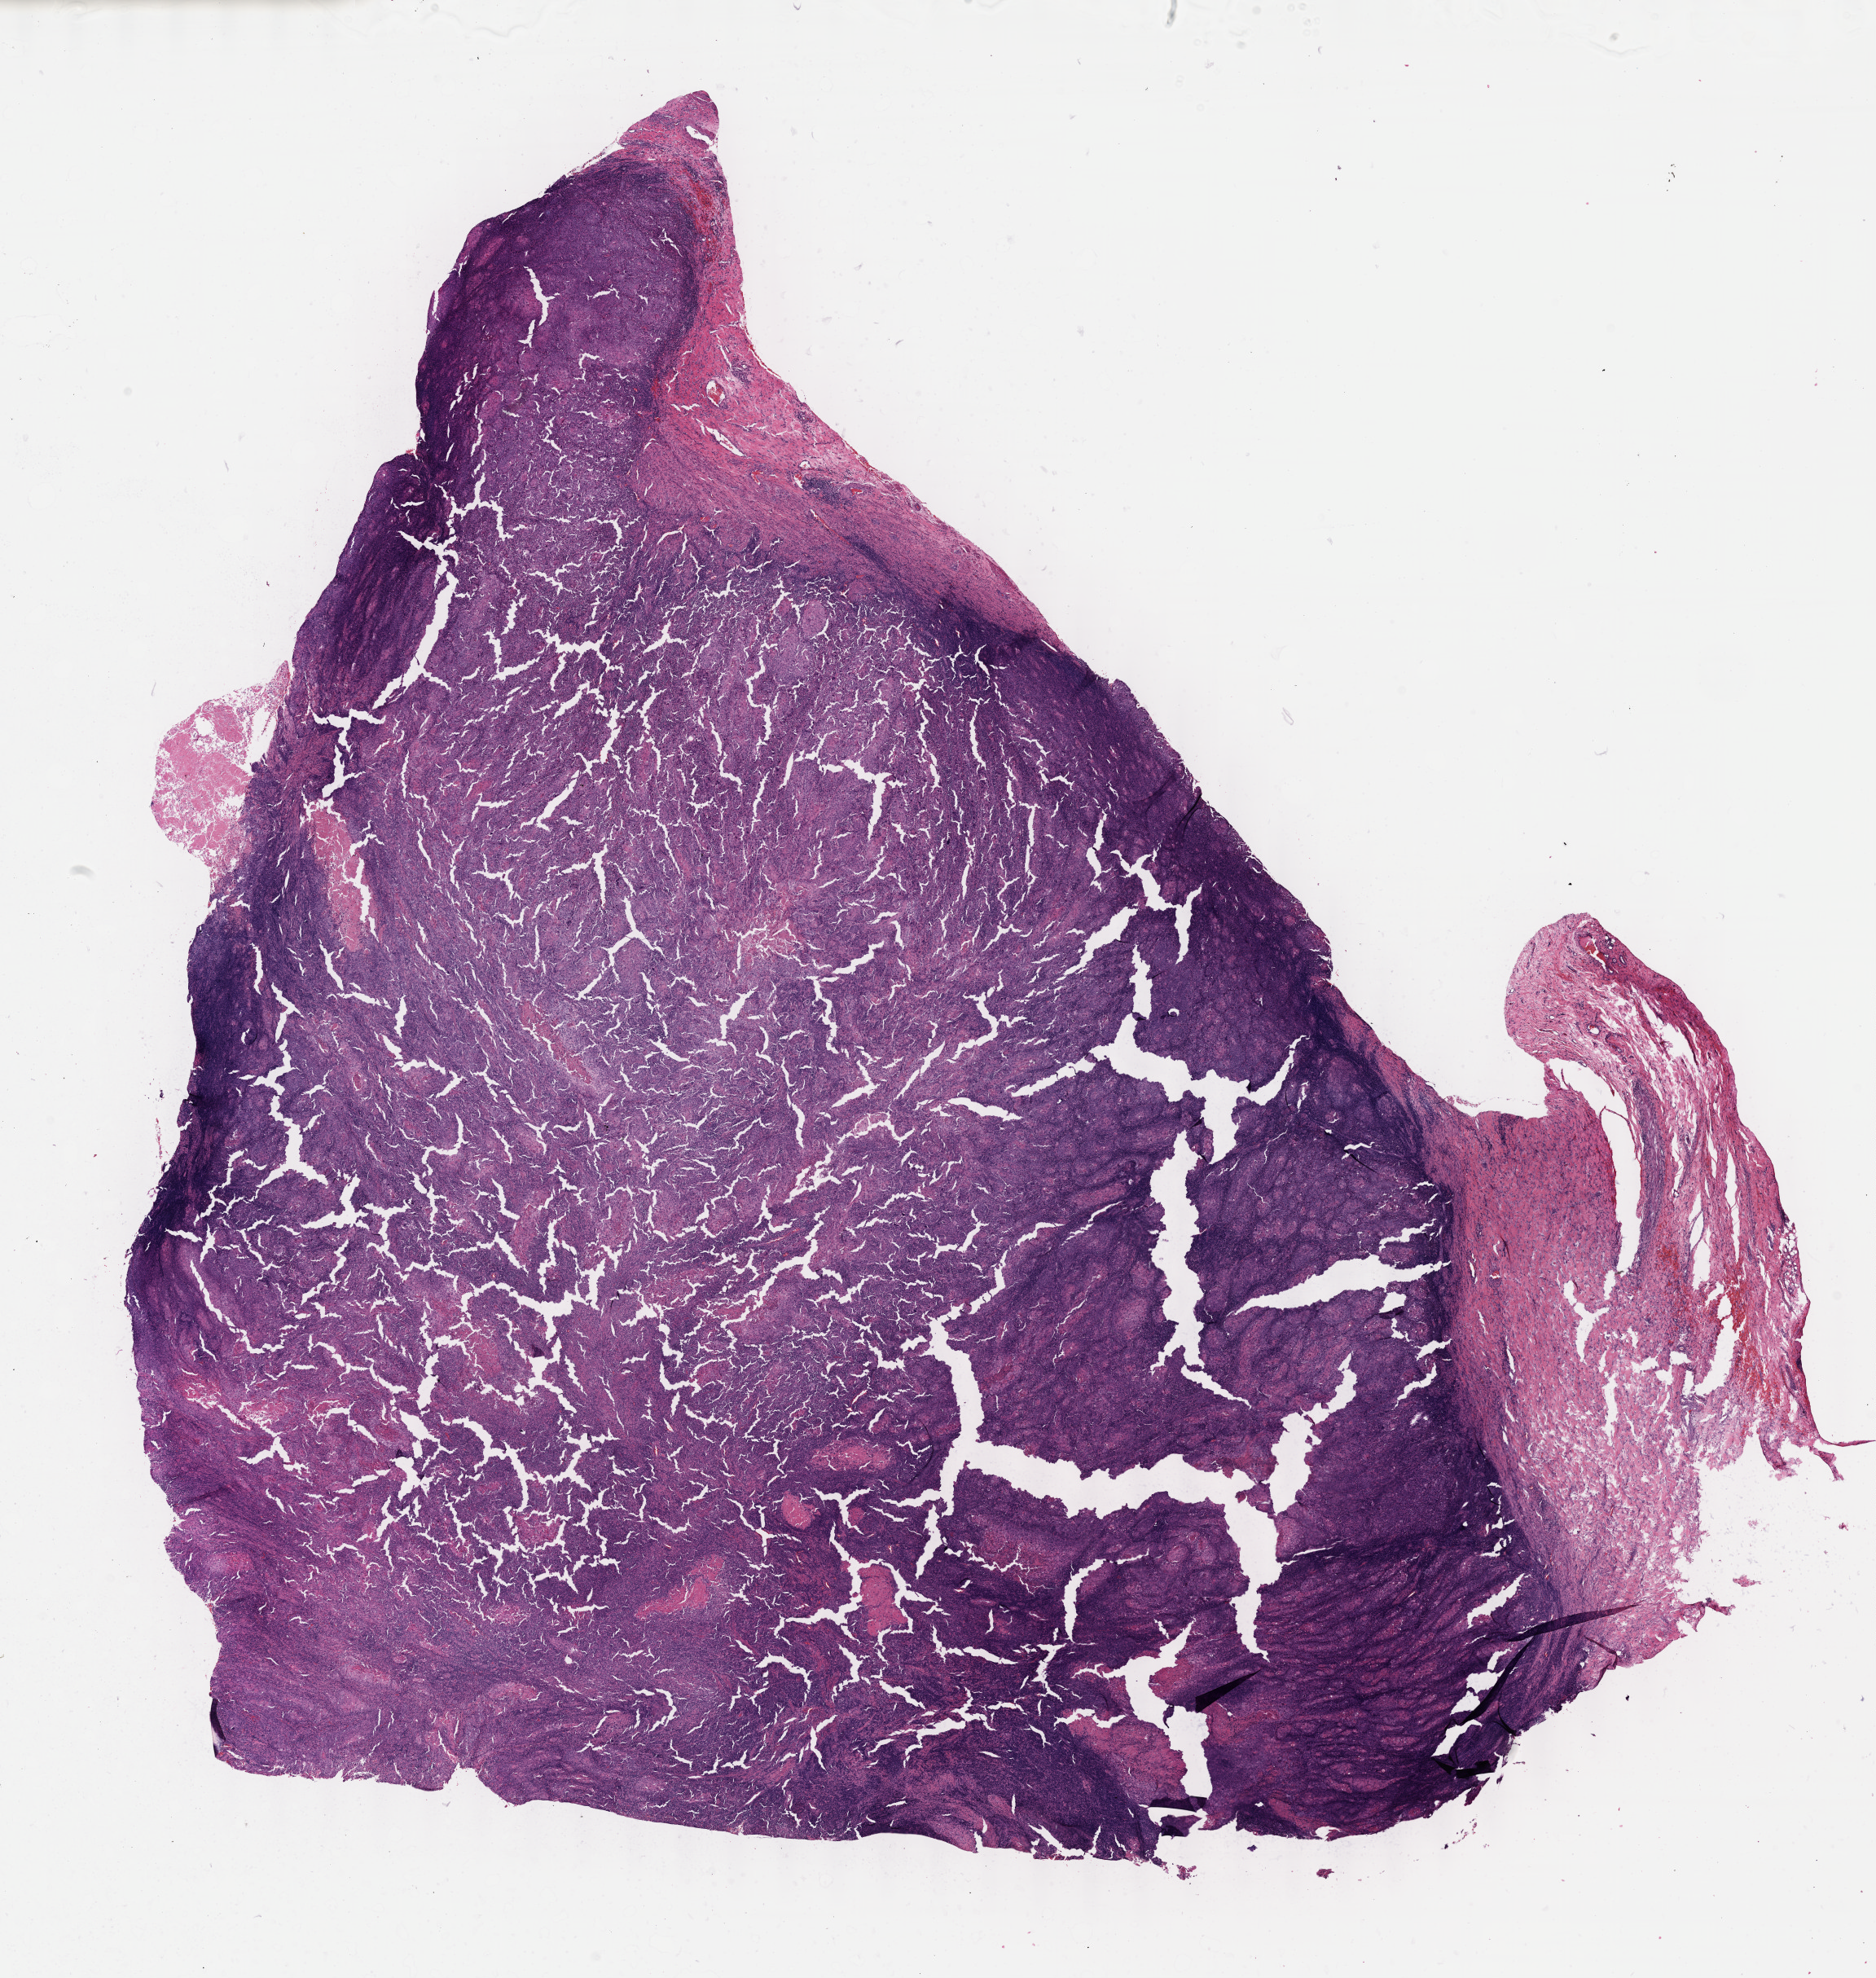
Digitized H&E tissue section (whole slide) — a low-resolution overview of the entire scanned area, about 18.6 x 19.6 mm (from a 40x scan); formalin-fixed paraffin-embedded (FFPE) diagnostic section; sample: primary tumour, esophagus. Male, age 57 years at initial diagnosis. Histologic grade: G1 (well differentiated).
Diagnosis: Squamous cell carcinoma, NOS (lower third of esophagus). Lymph nodes positive (case pathology): 0 of 11 examined. AJCC pathologic stage: IIA (7th edition).